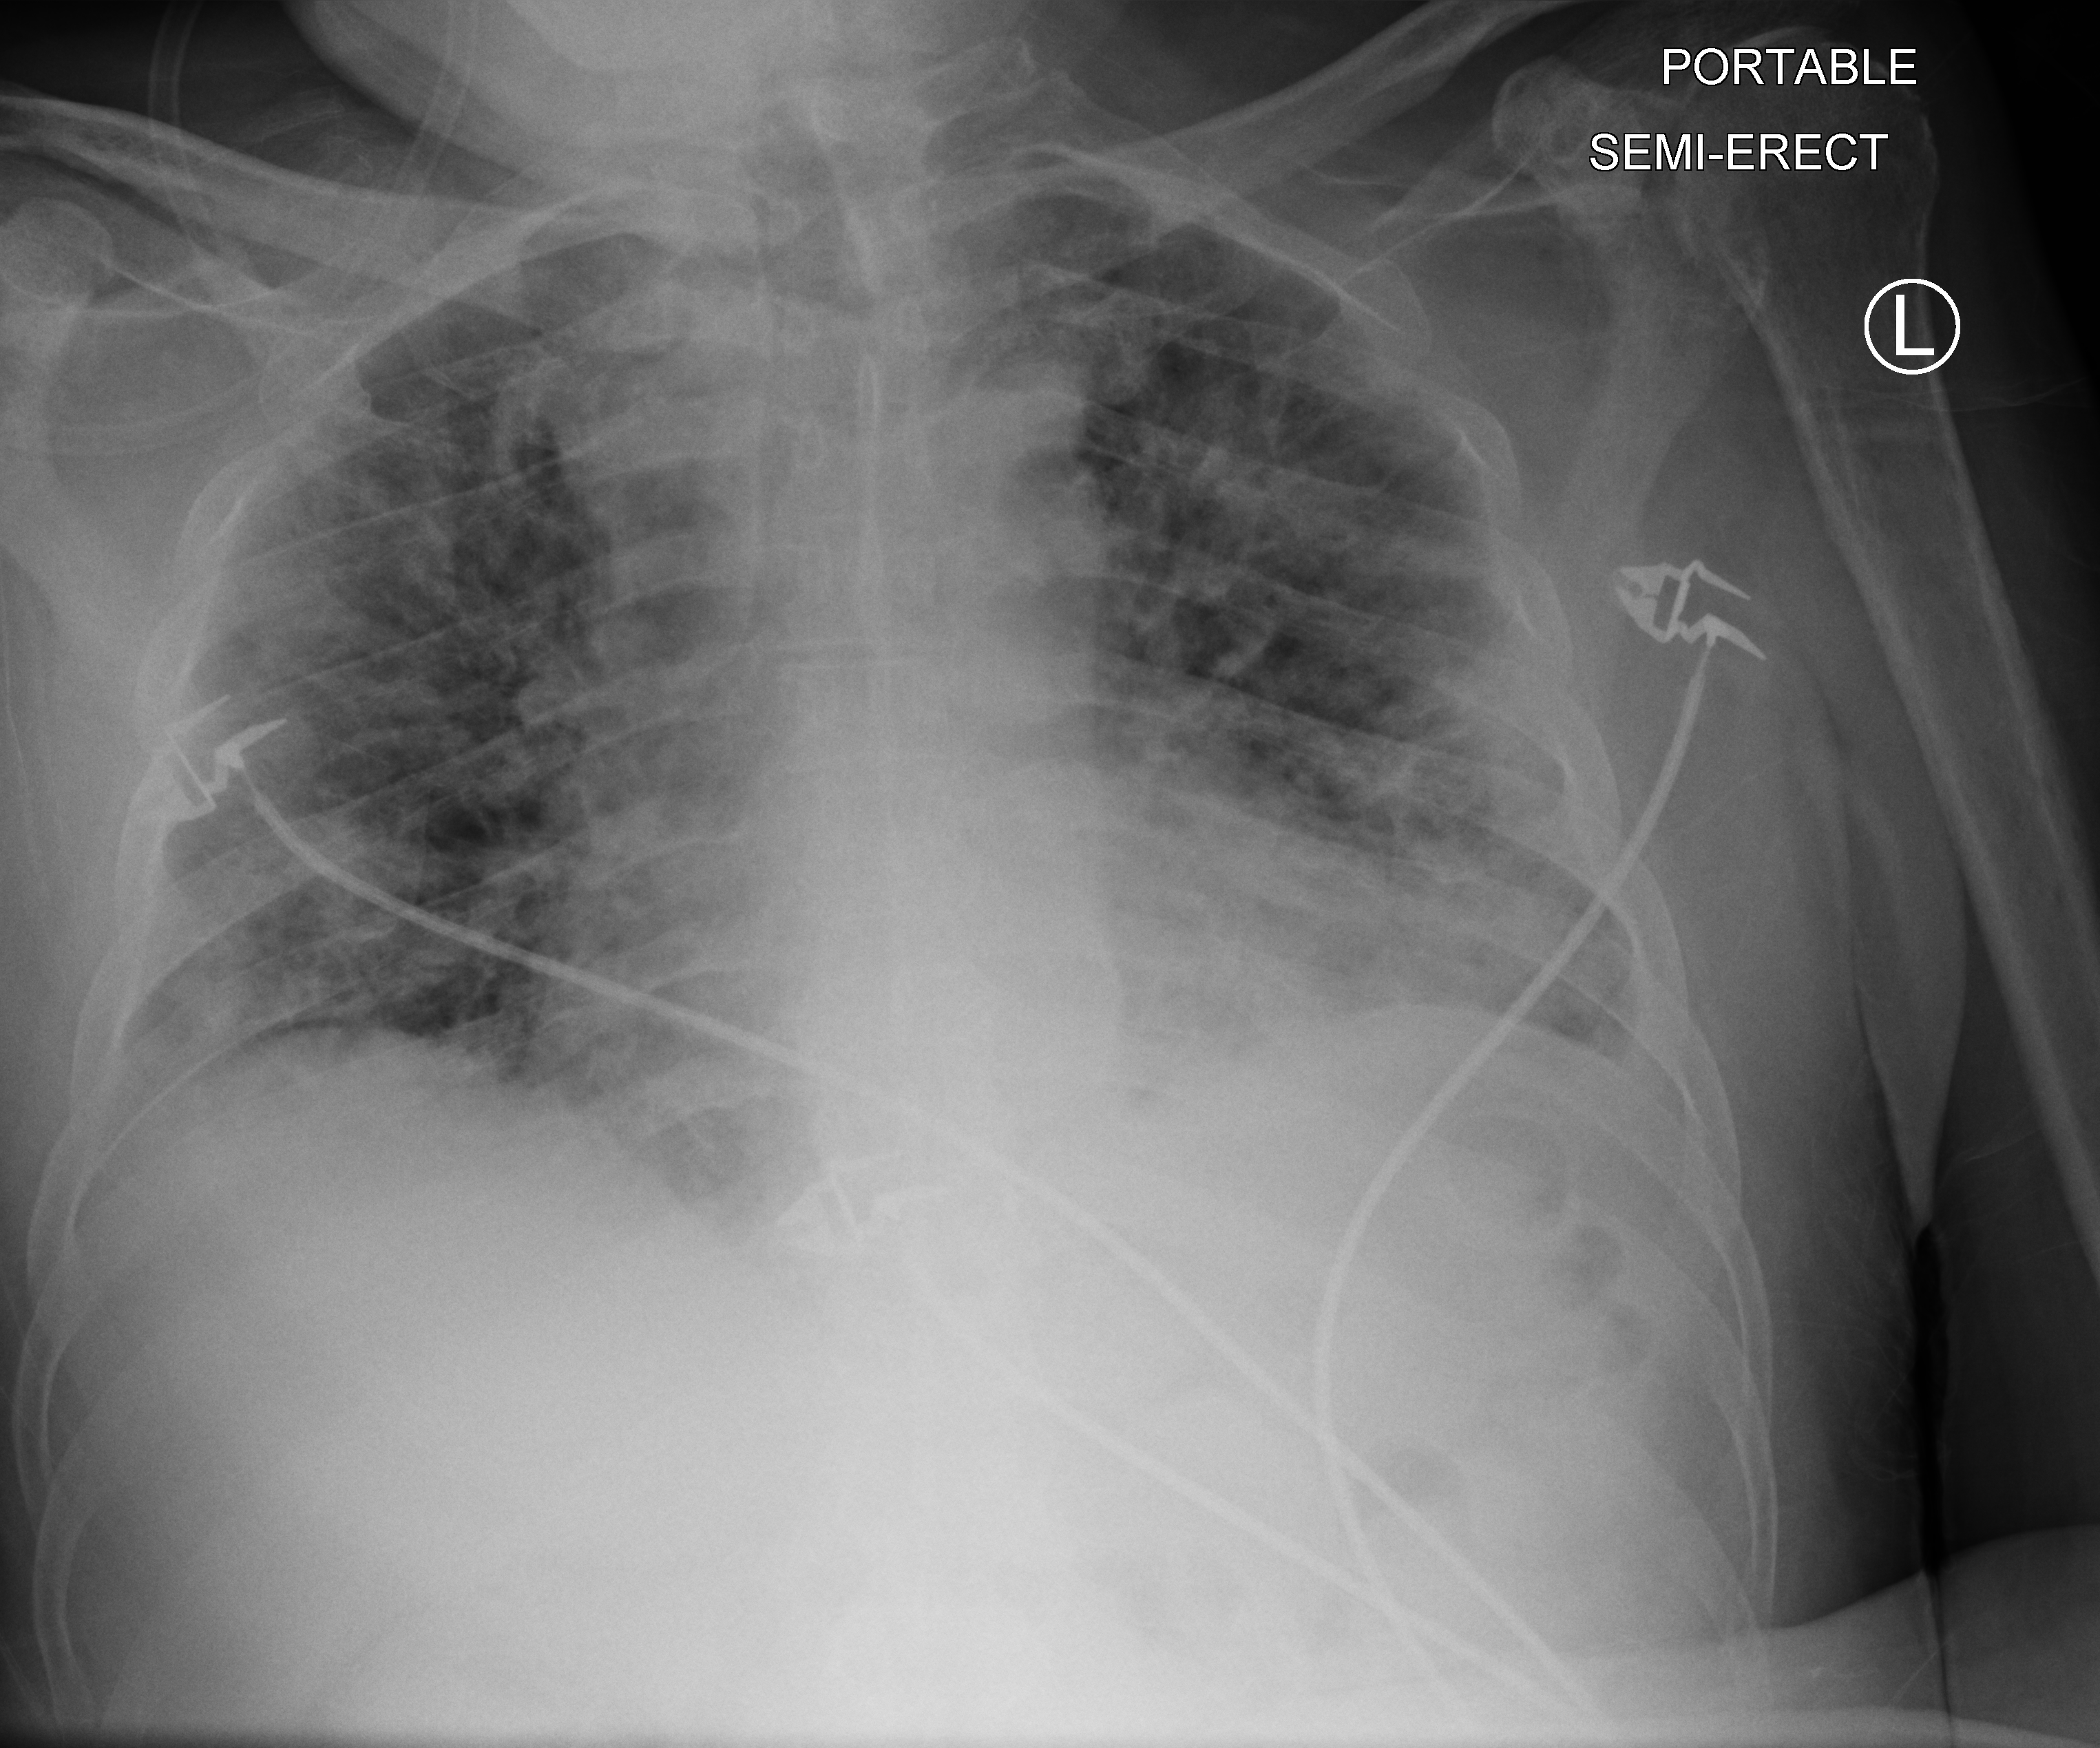
Portable chest radiograph, anteroposterior (AP) projection. Patient hospitalised with COVID-19; male, aged 60–74 years.
Admission-level facts for this patient (not findings on this image; timing relative to this image not recorded):
- mechanically ventilated during this hospital stay: no
- admitted to intensive care during this hospital stay: no